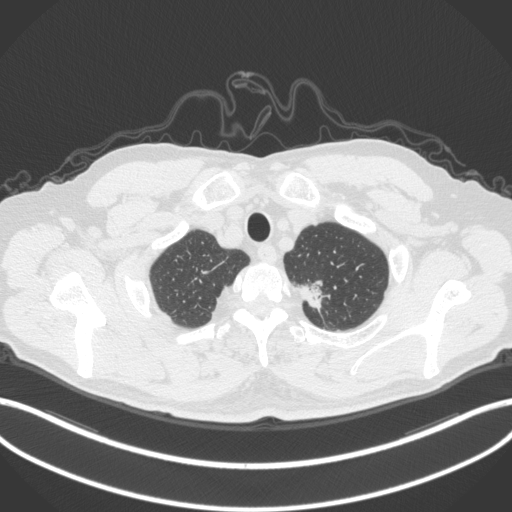
Chest CT, one axial slice. Slice 343 of 382 in the series (ordered by position). Reconstruction kernel B31f. Lung window (W 1500 / L -600 HU). 1 mm slice thickness. 512 × 512 image matrix, field of view 400 × 400 mm. Patient: male, 64 years. From the clinical record (not read from this slice): clinical TNM (as recorded): T1c N0 M0.
Outlined on this slice (bounding box drawn by a radiologist):
- lung tumour (recorded histology: adenocarcinoma): bounding box (x1, y1, x2, y2) in pixels: (298, 276, 333, 316)